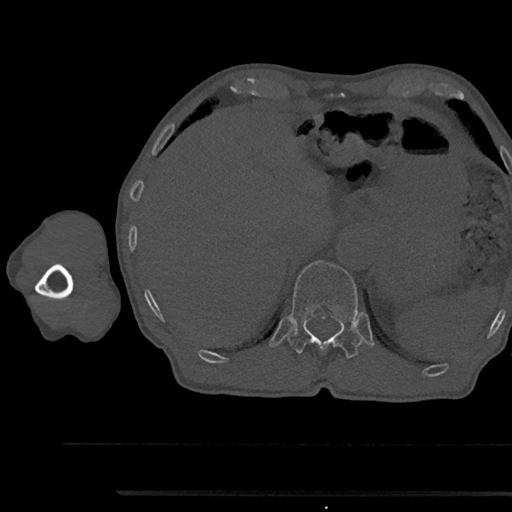
CT including the spine, one axial slice; position 722 of 797 along the scan axis; 120 kVp; bone window (W 1800 / L 400 HU); 512 × 512 image matrix, field of view 367 × 367 mm. Patient: male, 79 years. From the clinical record (not read from this slice): primary cancer: prostate.
Outlined on this slice (semi-automatically segmented with operator editing):
- T12 vertebra: bounding box <288,260,362,358> (left, top, right, bottom; pixels)